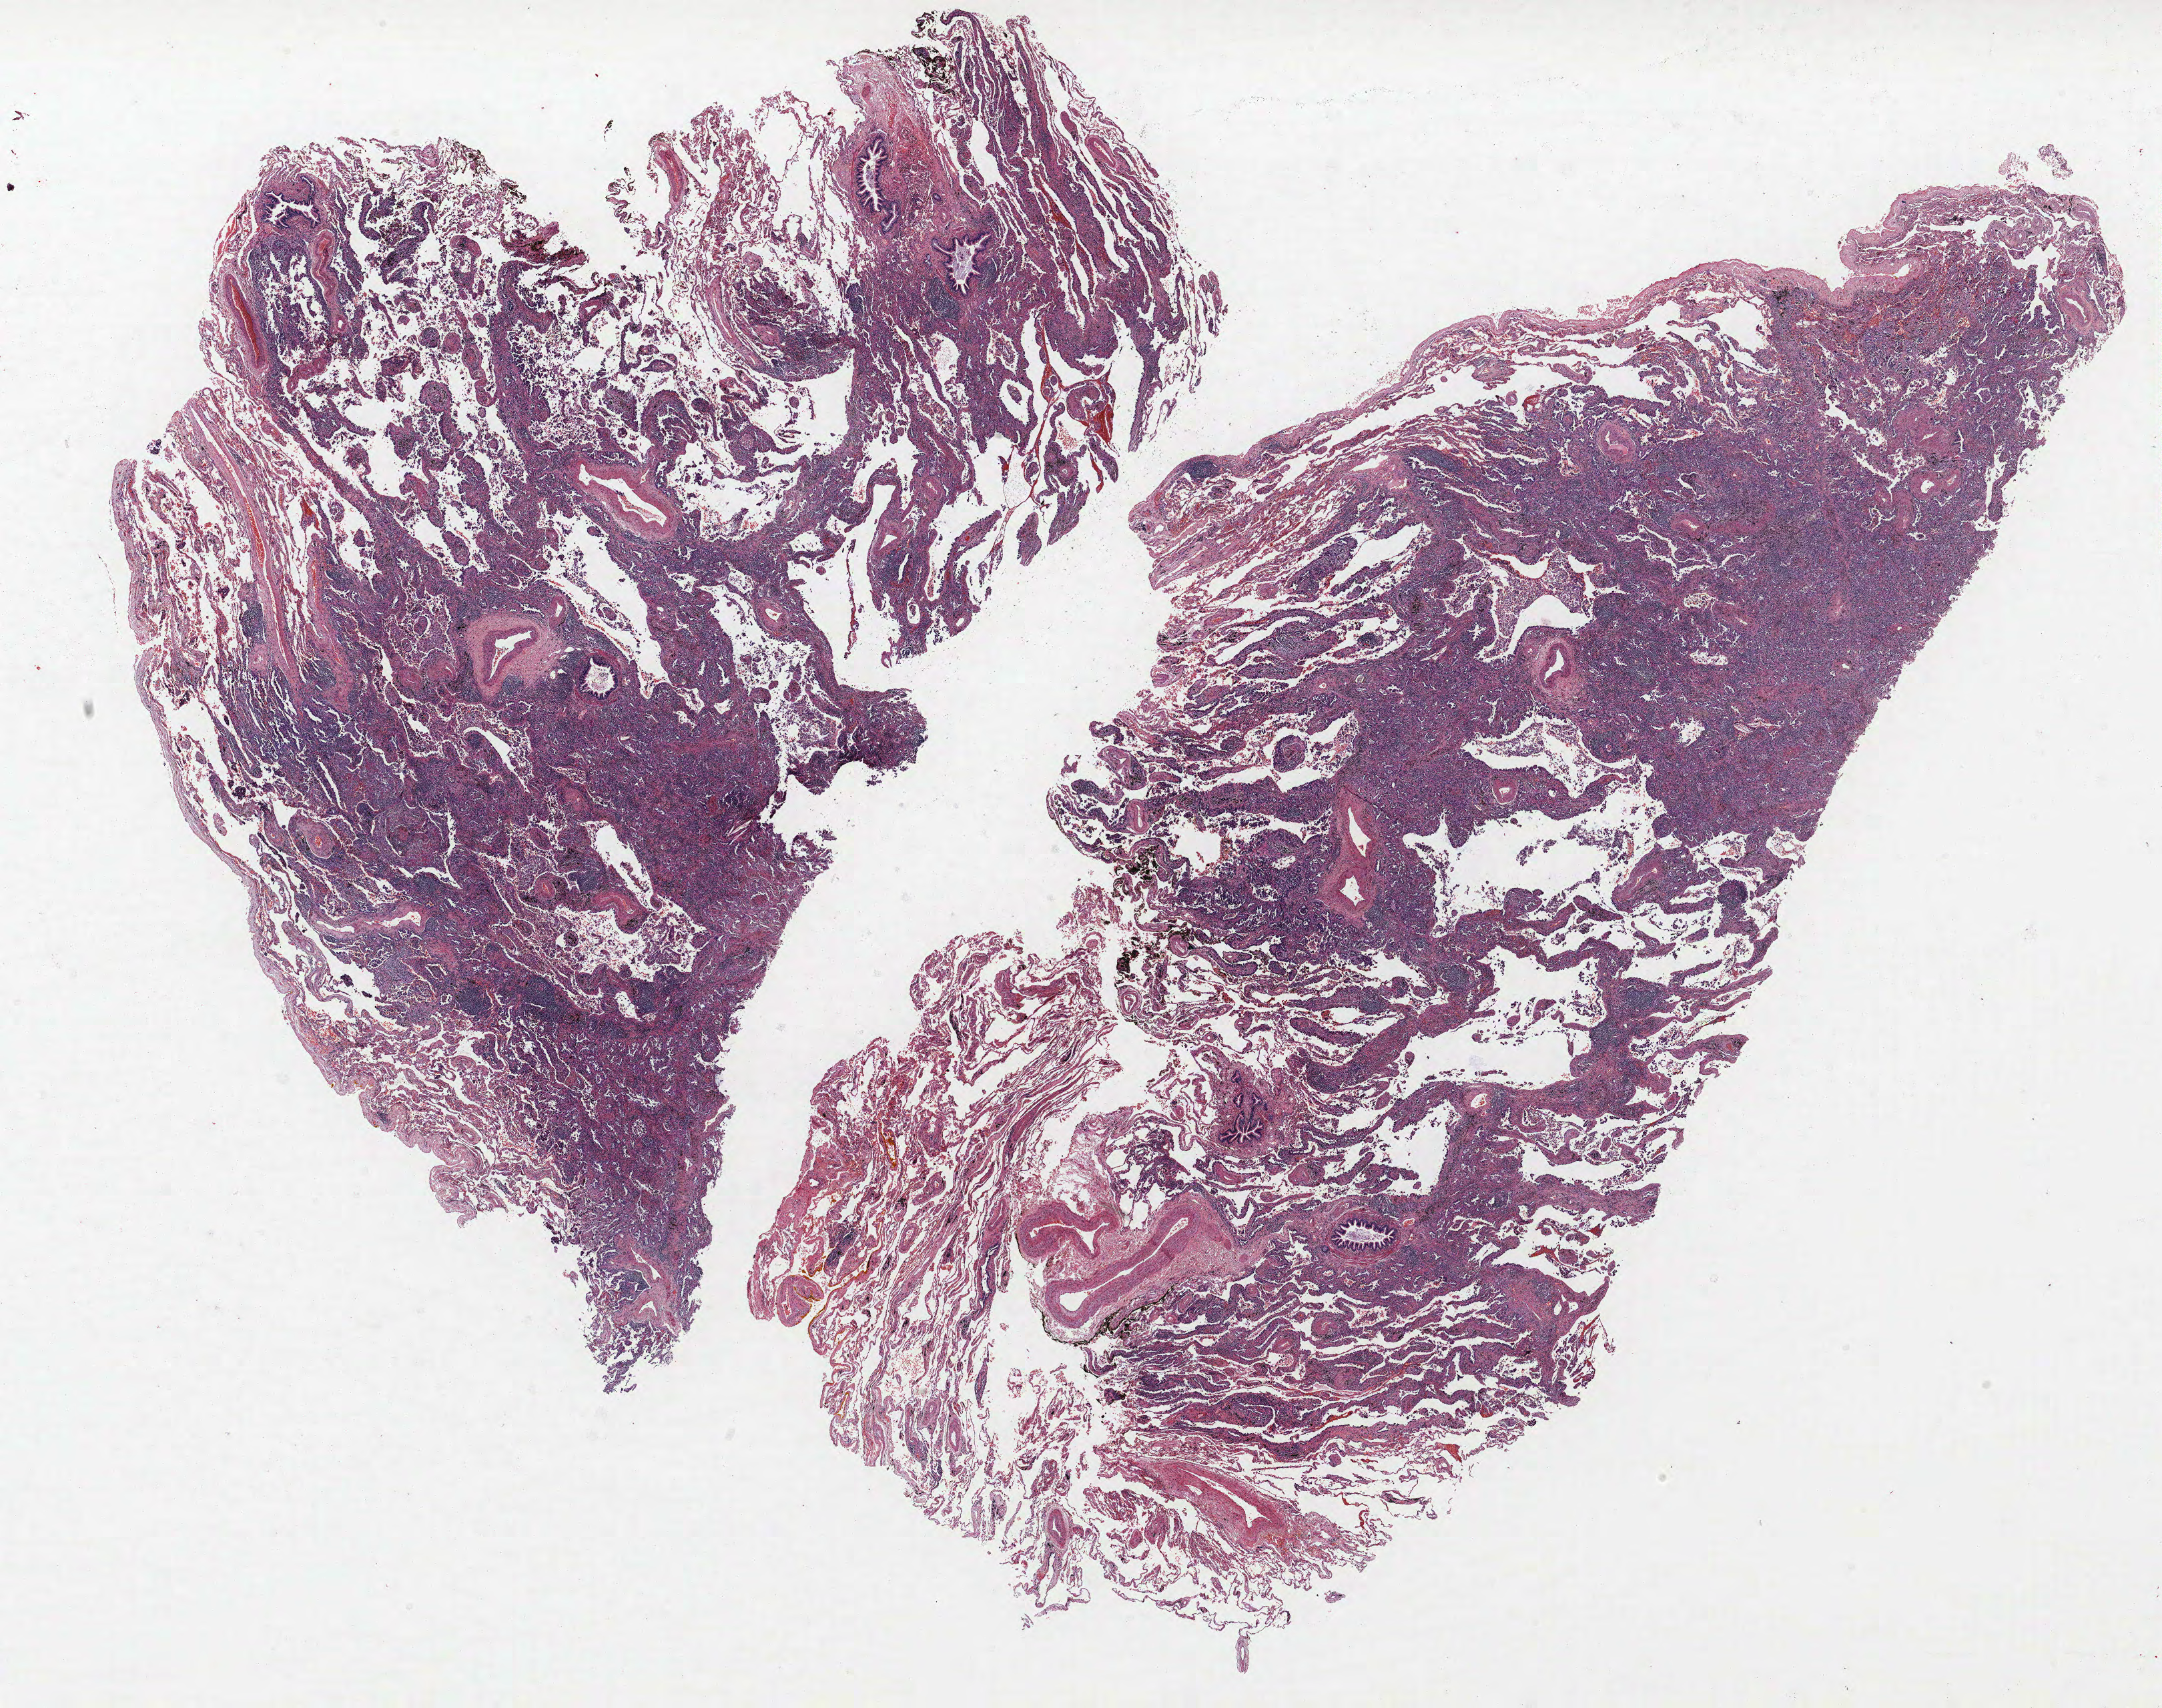
Whole-slide histology image, H&E-stained, shown as a low-resolution overview of the whole scanned area (about 25.9 x 20.5 mm); formalin-fixed paraffin-embedded (FFPE) section; lung tissue. Female patient, aged 65 at enrolment. Grade: moderately differentiated (G2).
Tumour size (pathology): 25 mm. Stage (AJCC 6th edition): IA. Primary tumour location (clinical record): right lower lobe. Participant's lung-cancer diagnosis: Adenocarcinoma, NOS (ICD-O-3 8140/3).